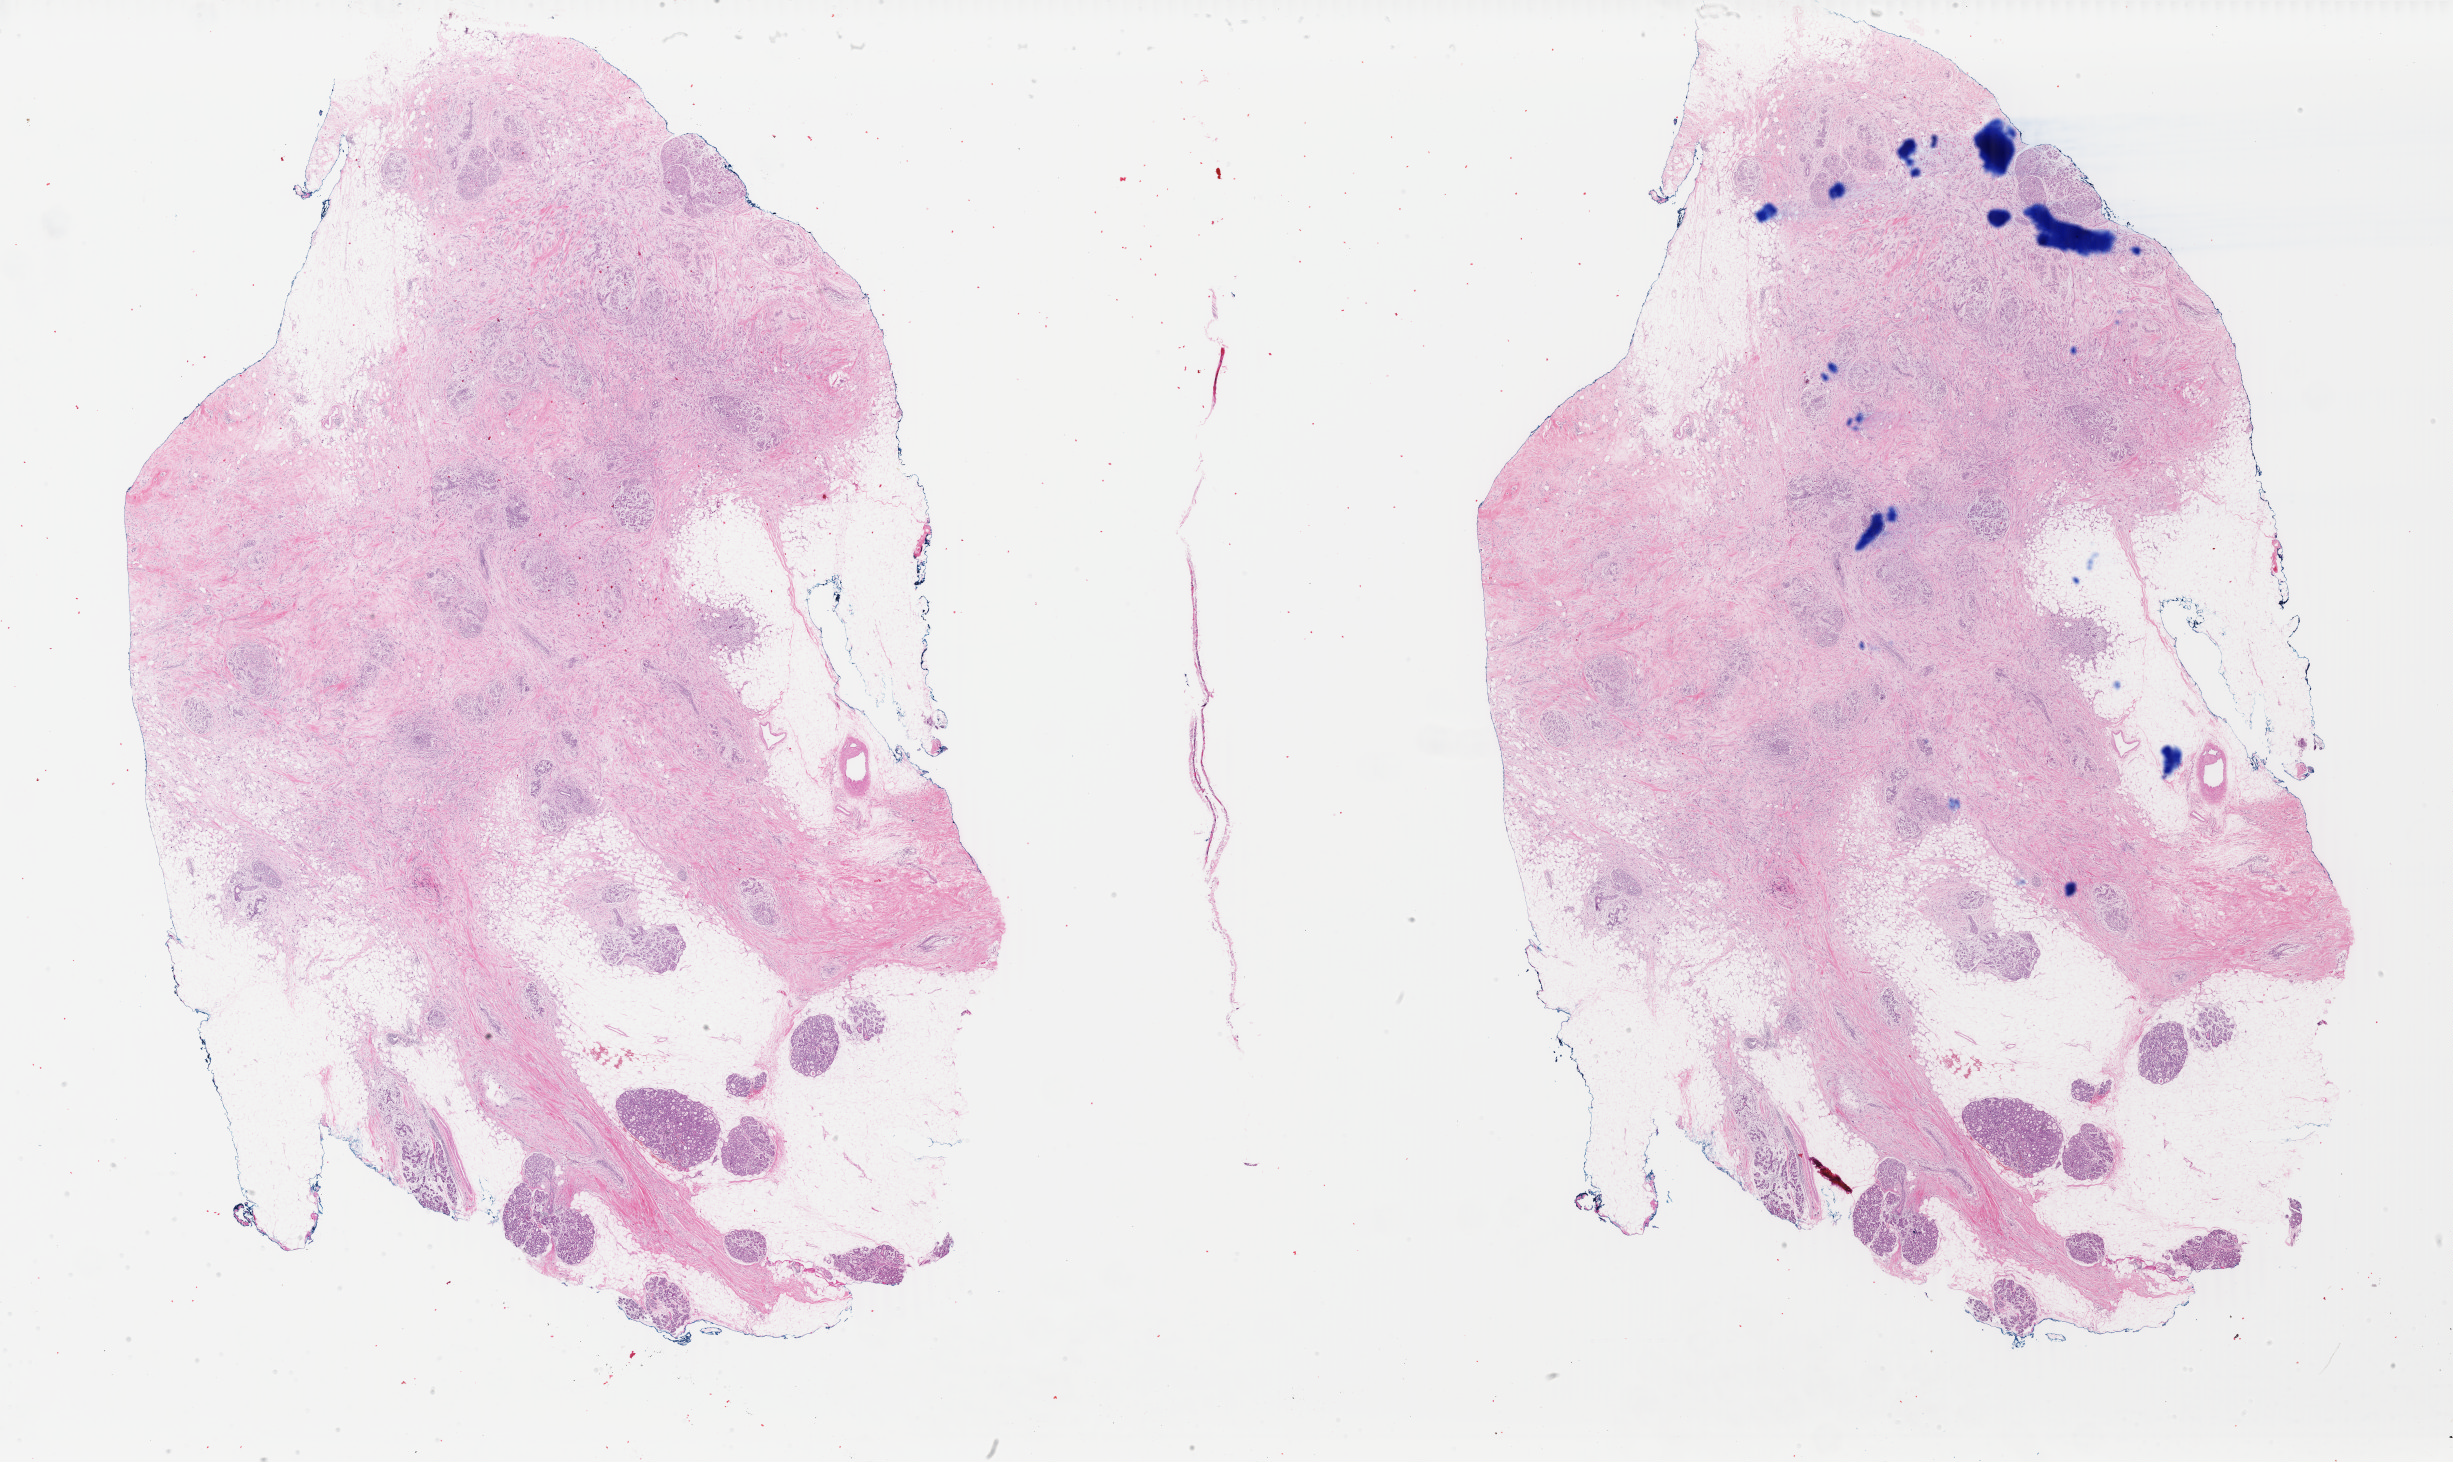
Hematoxylin and eosin (H&E) stained whole-slide image, low-resolution overview of the scanned area, about 39.0 x 23.3 mm. FFPE section. Breast, primary tumour sample. Female patient; age at initial diagnosis 40 years.
Lymph nodes positive (case pathology): 9 of 21 examined. Laterality: left. Pathologic diagnosis: Lobular carcinoma, NOS. AJCC pathologic stage: IIIA.